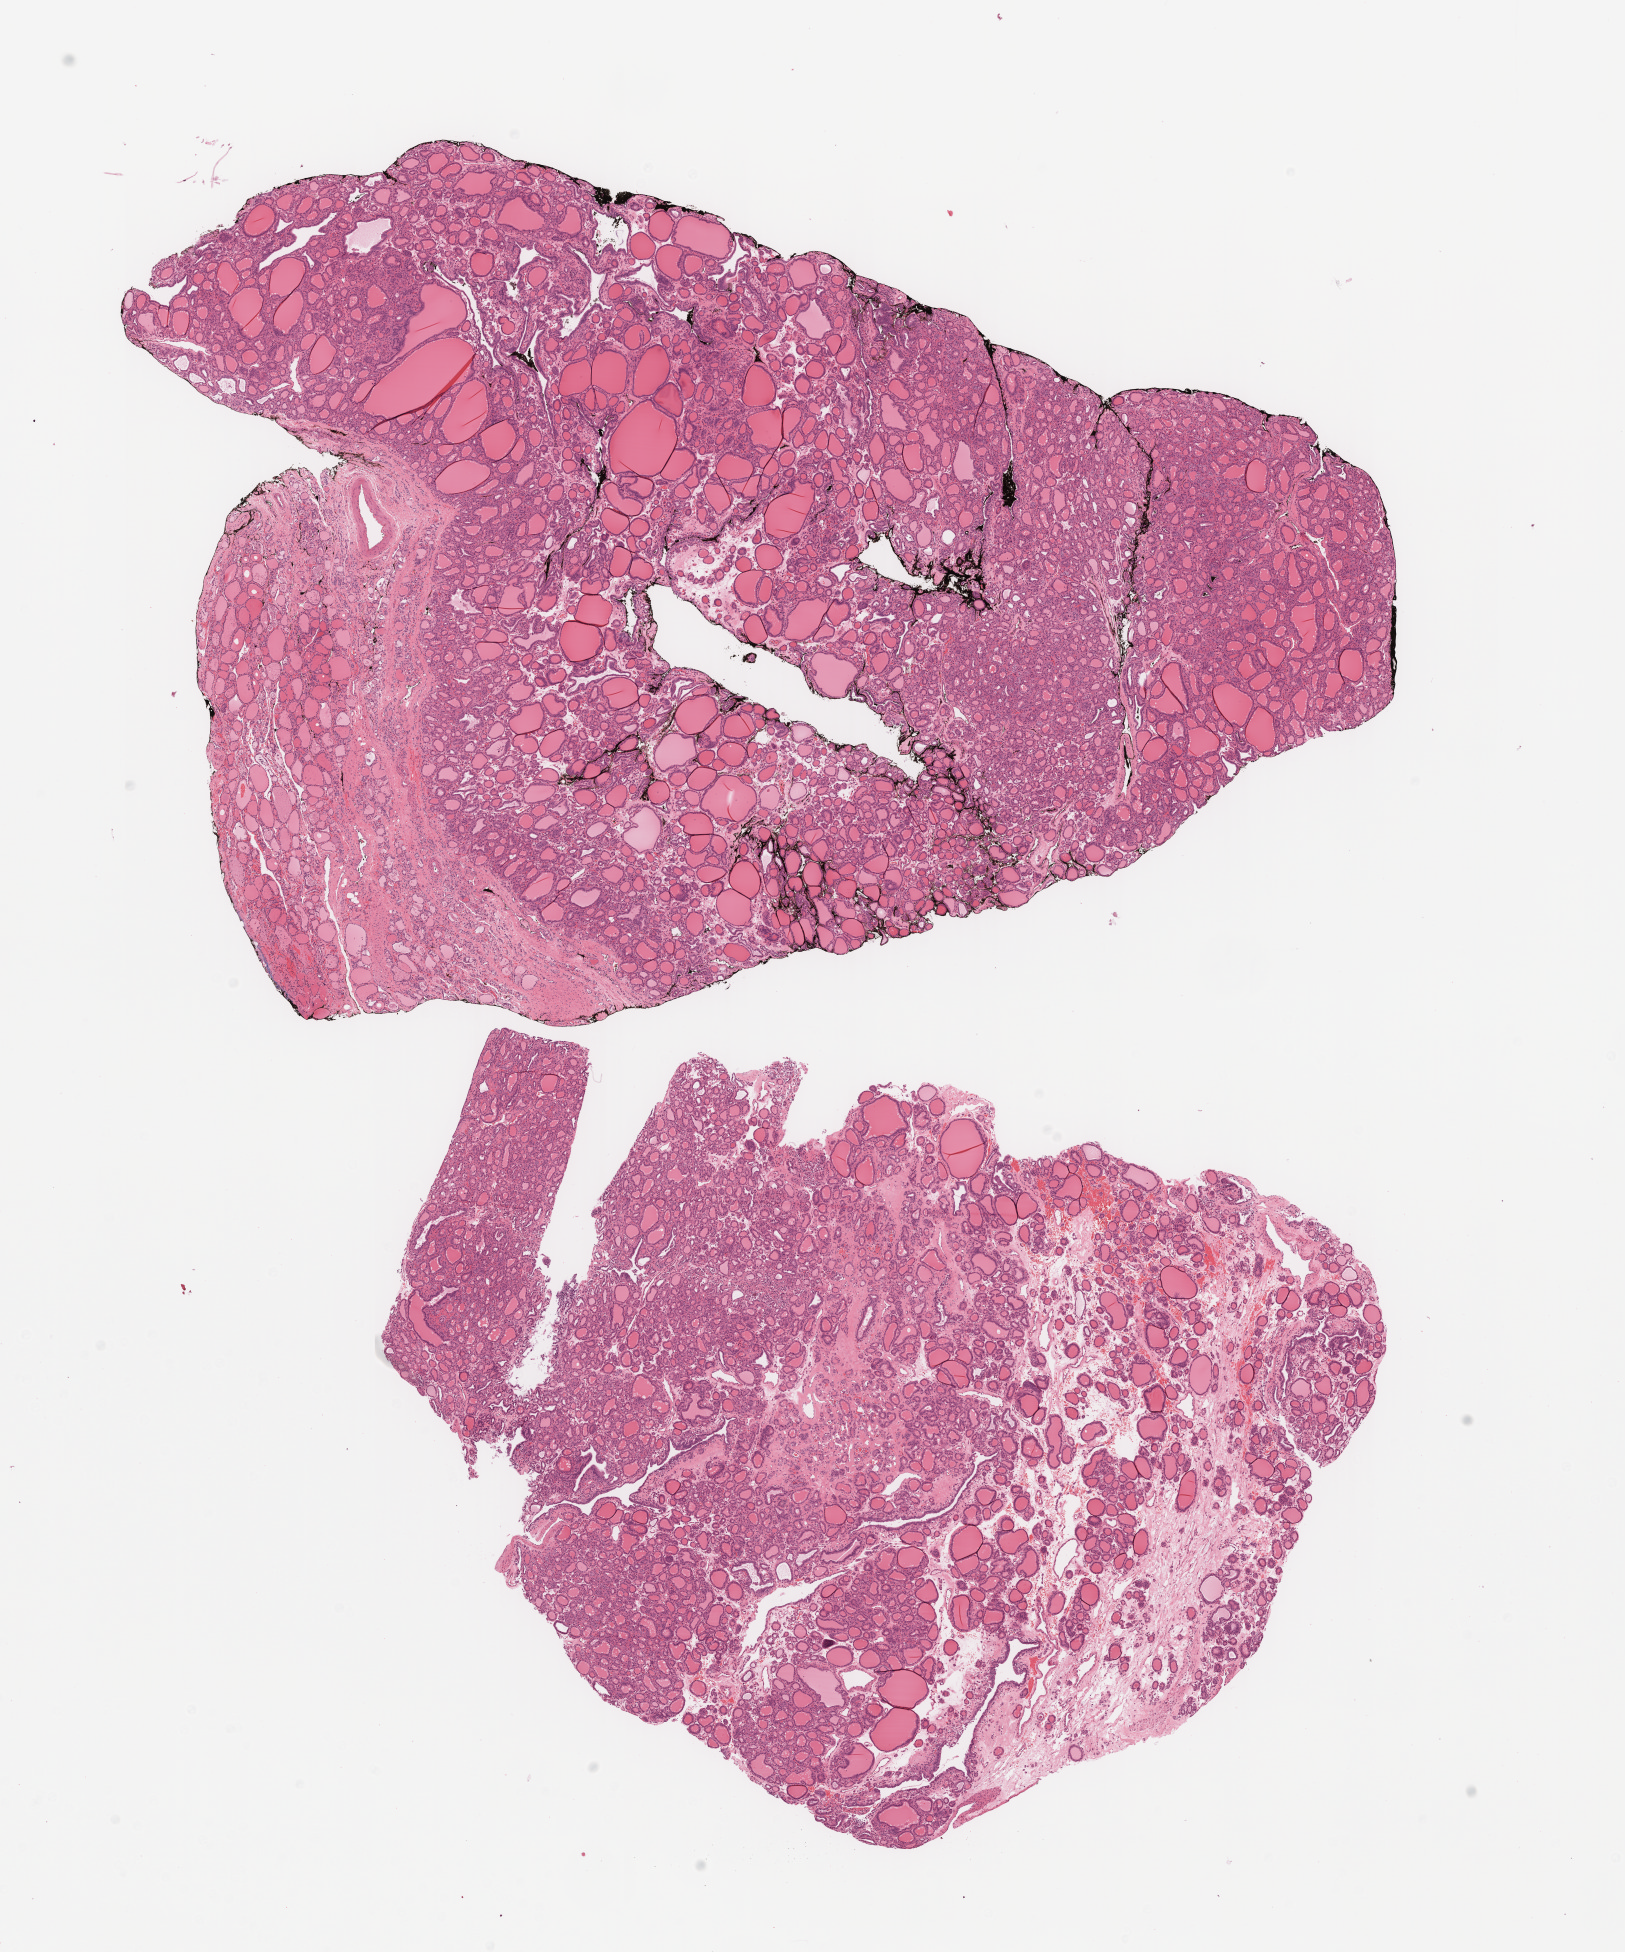
Hematoxylin and eosin (H&E) stained whole-slide image — whole scanned area (about 13.0 x 15.7 mm, from a 20x scan) shown as a low-resolution overview. Formalin-fixed paraffin-embedded (FFPE) diagnostic section. Sample: primary tumour, thyroid. Female, age 54 years at initial diagnosis.
TNM: T2 NX MX. AJCC pathologic stage: II. Laterality: right. Pathologic diagnosis: Papillary carcinoma, follicular variant (thyroid gland).